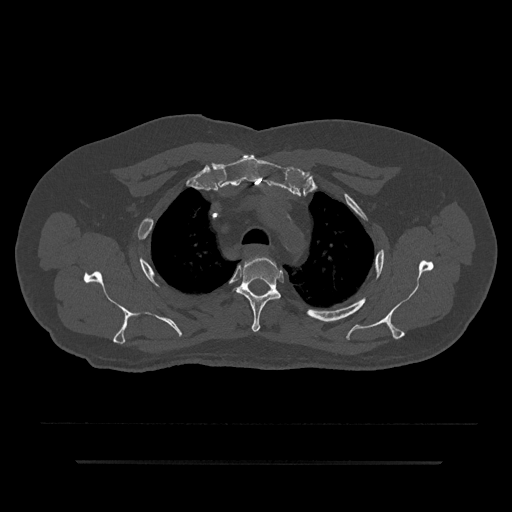
CT including the spine, one axial slice. Position 656 of 797 along the scan axis. Reconstruction kernel Br40s/3. 120 kVp. Bone window (W 1800 / L 400 HU). 0.5 mm slice thickness. 512 × 512 image matrix. Male patient, age 59 years. Case-level facts recorded for this patient, not image findings: primary cancer: bile ducts; vertebrae with lytic lesions (as recorded): T10.
Annotated regions visible in this slice (semi-automatic segmentation, software-assisted and operator-edited):
- T3 vertebra: bounding box [x1, y1, x2, y2] px = [235, 256, 281, 332]